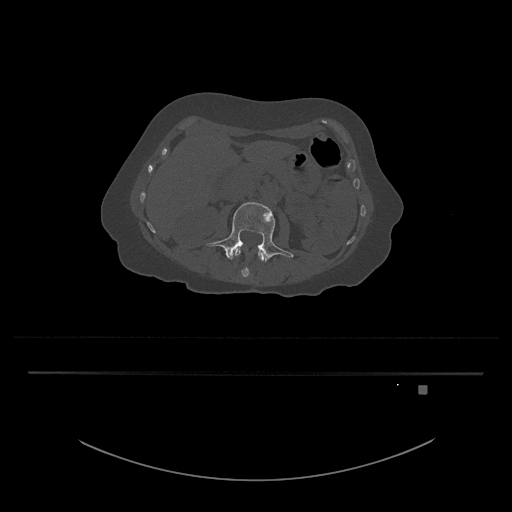
CT including the spine, one axial slice; slice 442 of 797 in the series (ordered by position); reconstruction kernel Br40s/3; 120 kVp; bone window (W 1800 / L 400 HU); 0.5 mm slice thickness; 512 × 512 image matrix, field of view 500 × 500 mm. Female patient, age 57 years. Case-level facts recorded for this patient, not image findings: primary cancer: cervical.
Outlined on this slice (semi-automatically segmented with operator editing):
- L3 vertebra: bounding box (x1, y1, x2, y2) in pixels: (206, 202, 294, 263)